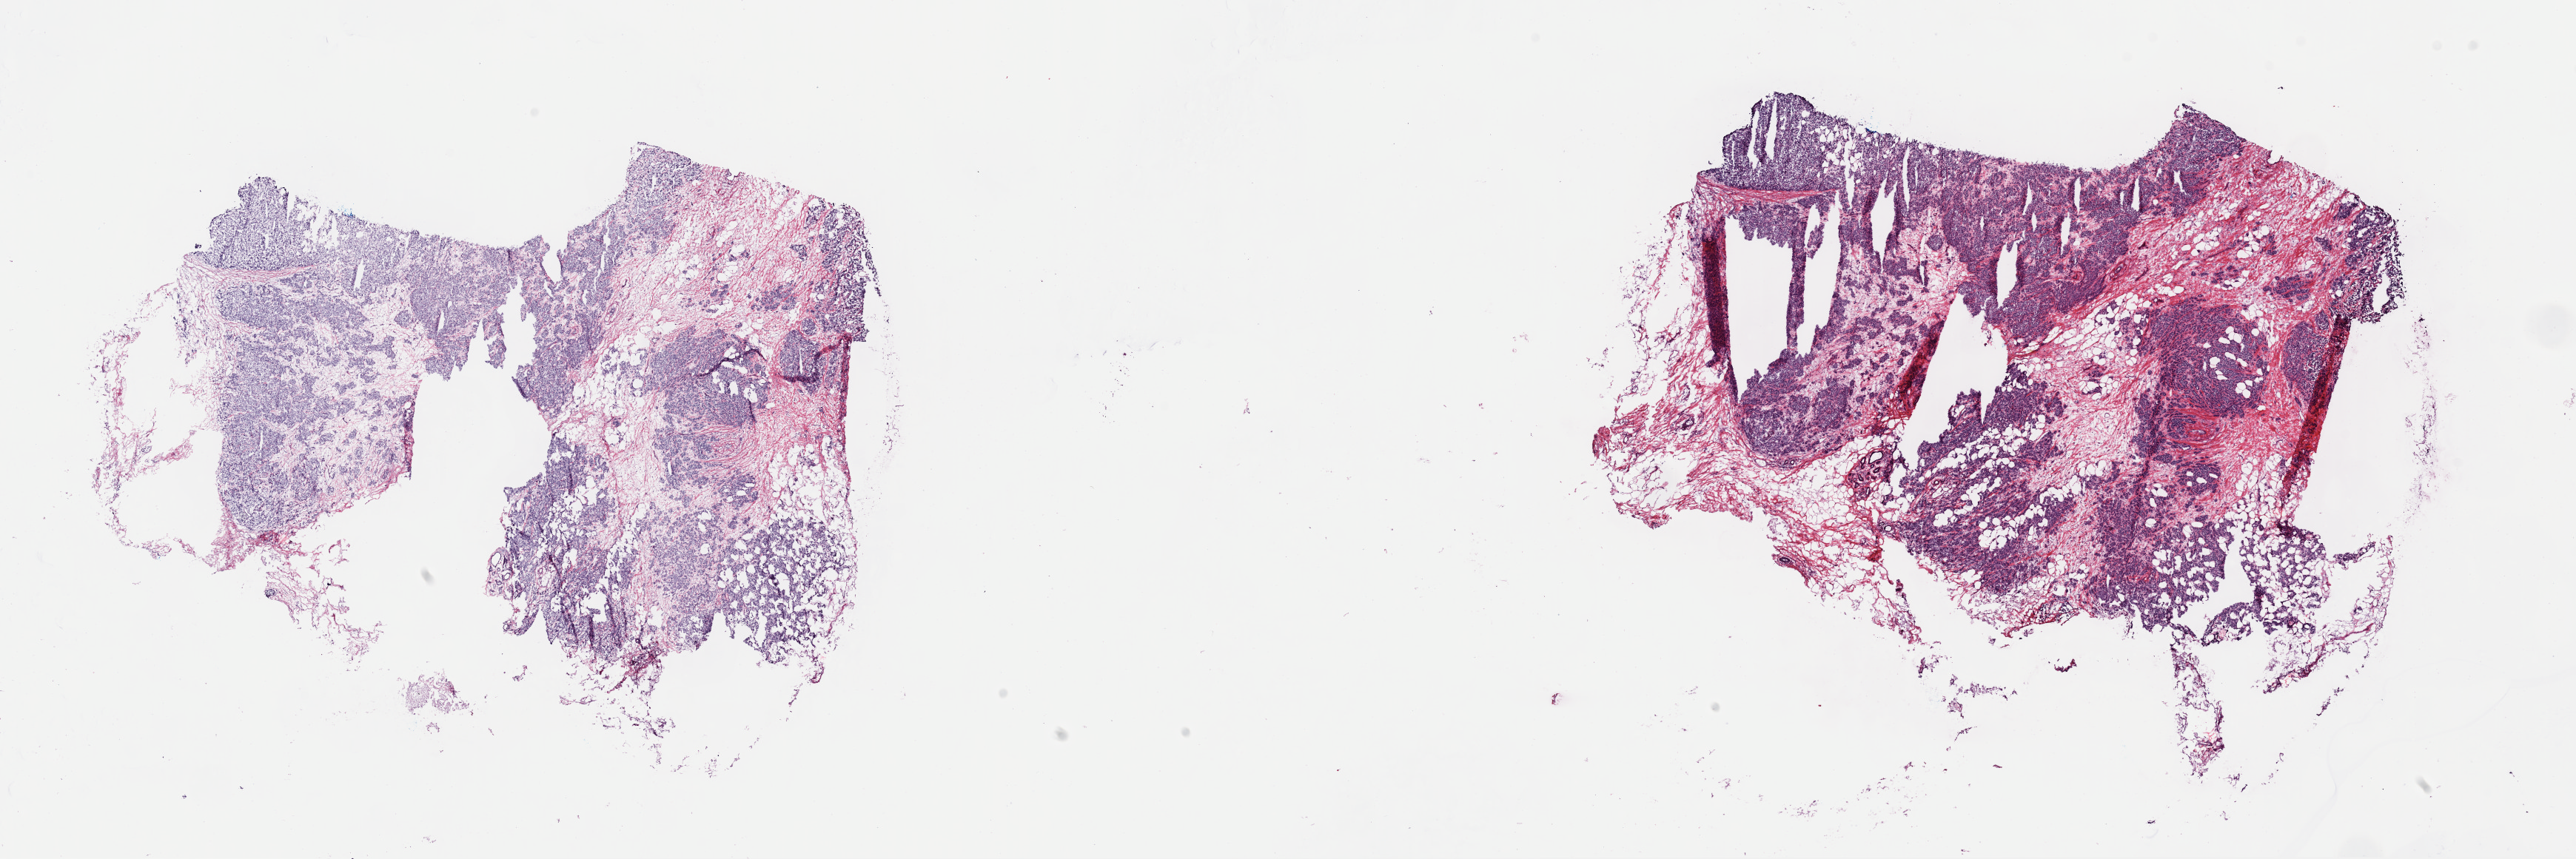
Digitized H&E-stained tissue section (whole slide) — a low-resolution overview of the entire scanned area, about 27.5 x 9.2 mm (slide scanned at 40x), frozen section from the top of the tissue portion, breast, primary tumour sample. Female, age 87 years at initial diagnosis. Pathologist review of this section (percent, as recorded): tumour cells 60%, tumour nuclei 80%, normal cells 34%, stromal cells 5%, necrosis 1%. Infiltration values recorded for this section: lymphocyte infiltration 2%, monocyte infiltration 0%, neutrophil infiltration 0%.
* AJCC pathologic stage: IIB (6th edition)
* histologic diagnosis: Lobular carcinoma, NOS
* lymph nodes positive (case pathology): 0 of 2 examined